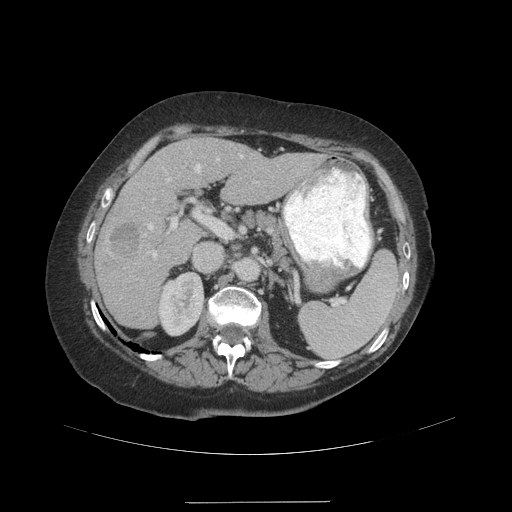
Contrast-enhanced abdominal CT (liver protocol), one axial slice; slice 61 of 99 in the series (ordered by position); reconstruction kernel STANDARD; 140 kVp; soft-tissue window (W 400 / L 40 HU); 2.5 mm slice thickness; 512 × 512 image matrix, field of view 440 × 440 mm. From the clinical record (not read from this slice): diagnosis: hepatocellular carcinoma (patient treated with transarterial chemoembolisation; whether this scan precedes or follows treatment is not stated here); TNM stage (as recorded): Stage-IVA; Child-Pugh class: A; tumour nodularity: multinodular.
Annotated regions visible in this slice (semi-automatic segmentation, software-assisted and operator-edited):
- liver parenchyma outside the tumour (the mass and vessels are separate outlines, so this box may not span the whole liver): bounding box <94,138,323,328> (left, top, right, bottom; pixels)
- mass: <108,223,140,258>
- liver vessels: <147,155,243,258>